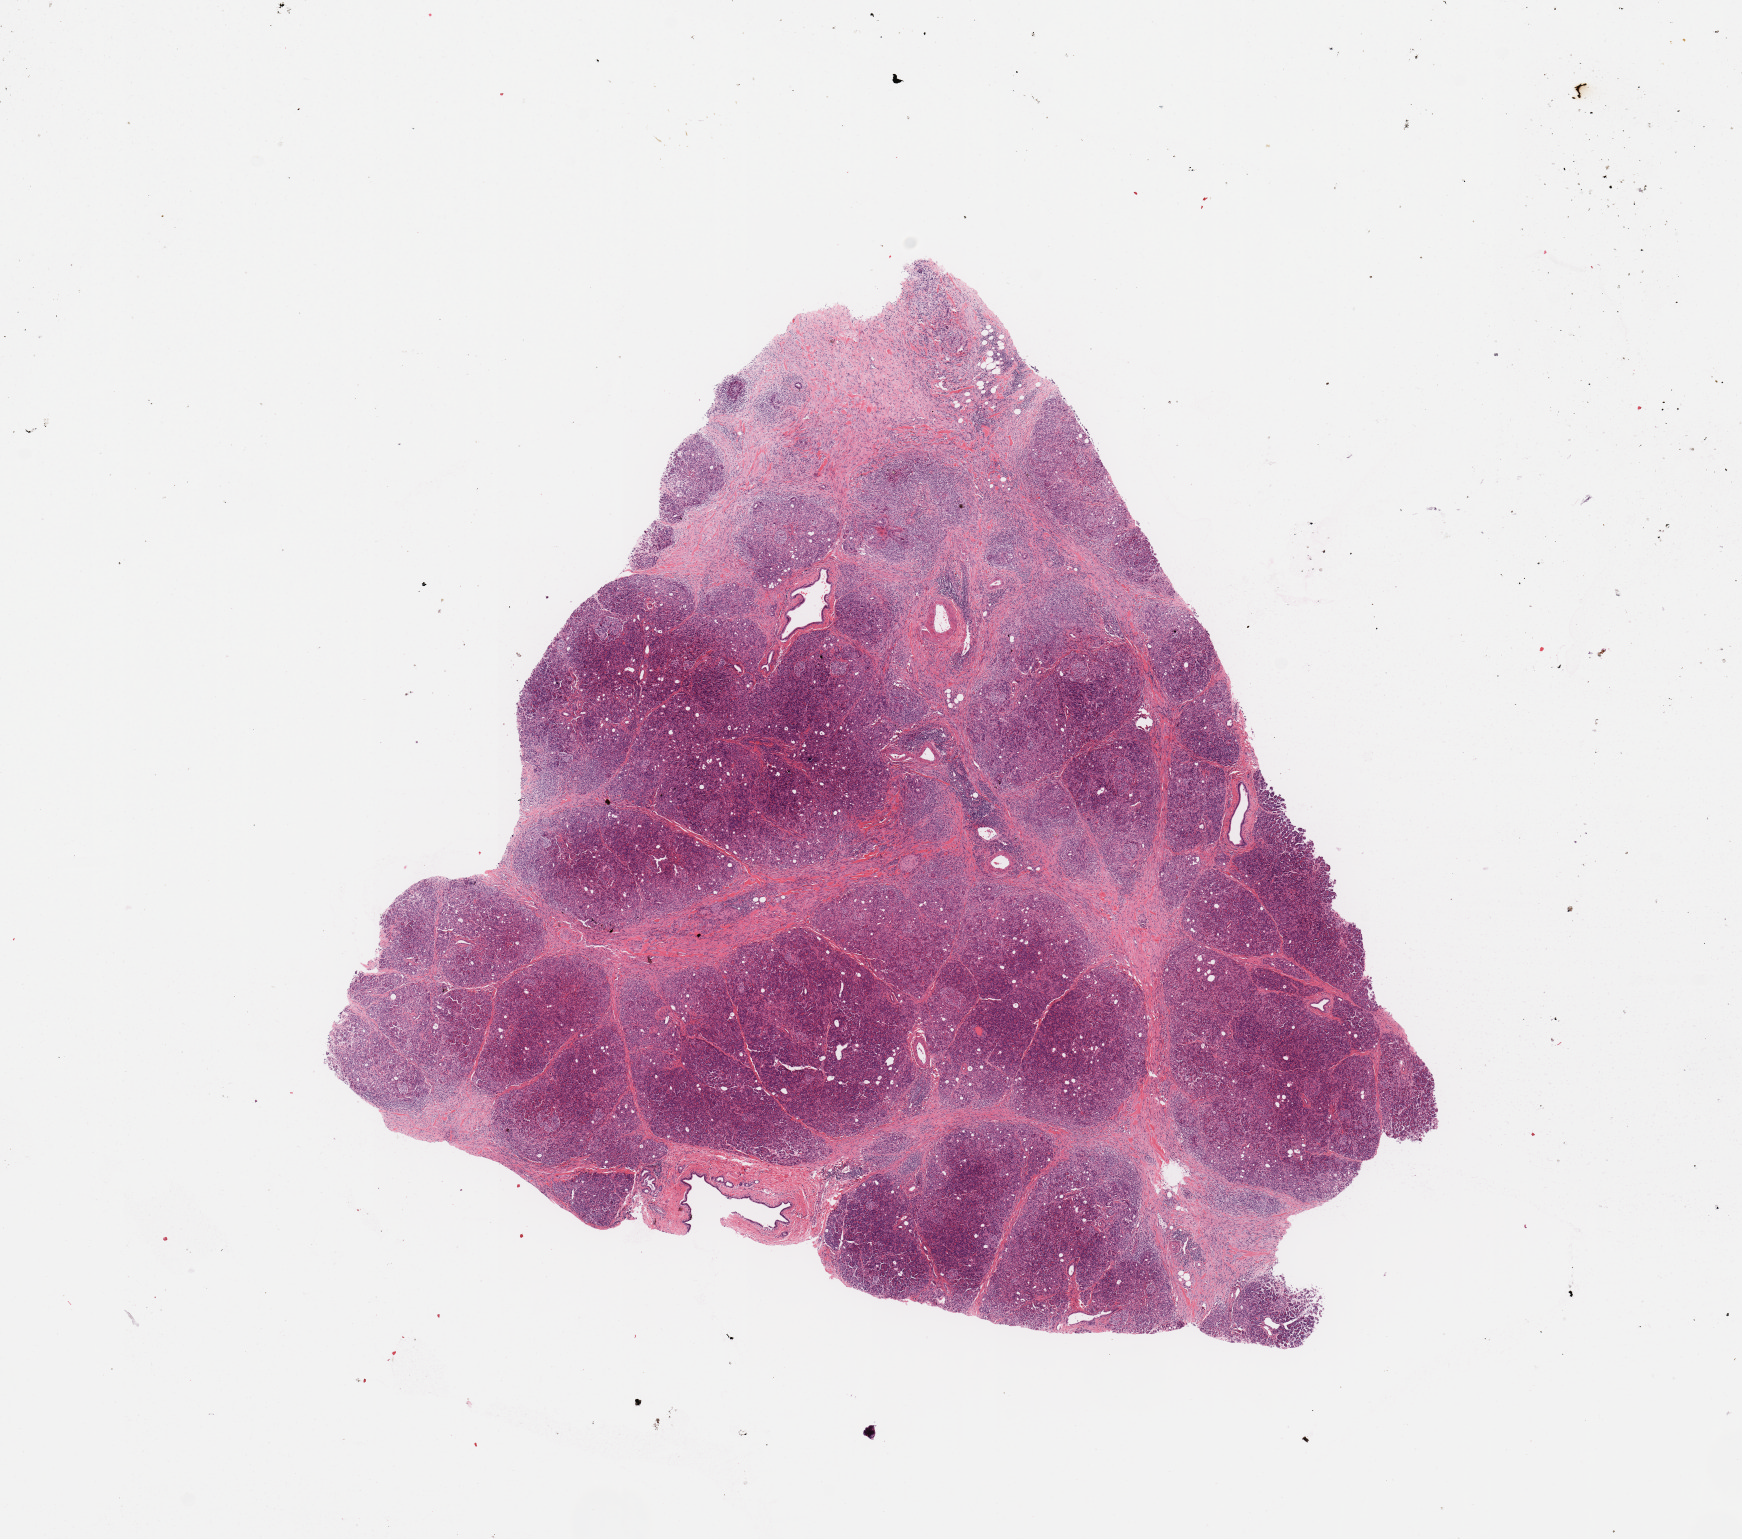
Digitized Hematoxylin and eosin (H&E) stained tissue section (whole slide), shown as a low-resolution overview of the whole scanned area (about 13.8 x 12.2 mm); pancreas, normal (non-tumour) tissue. Male, 31 y/o.
This section: normal (non-tumour) tissue from the same patient. Patient diagnosis: Infiltrating duct carcinoma, NOS.